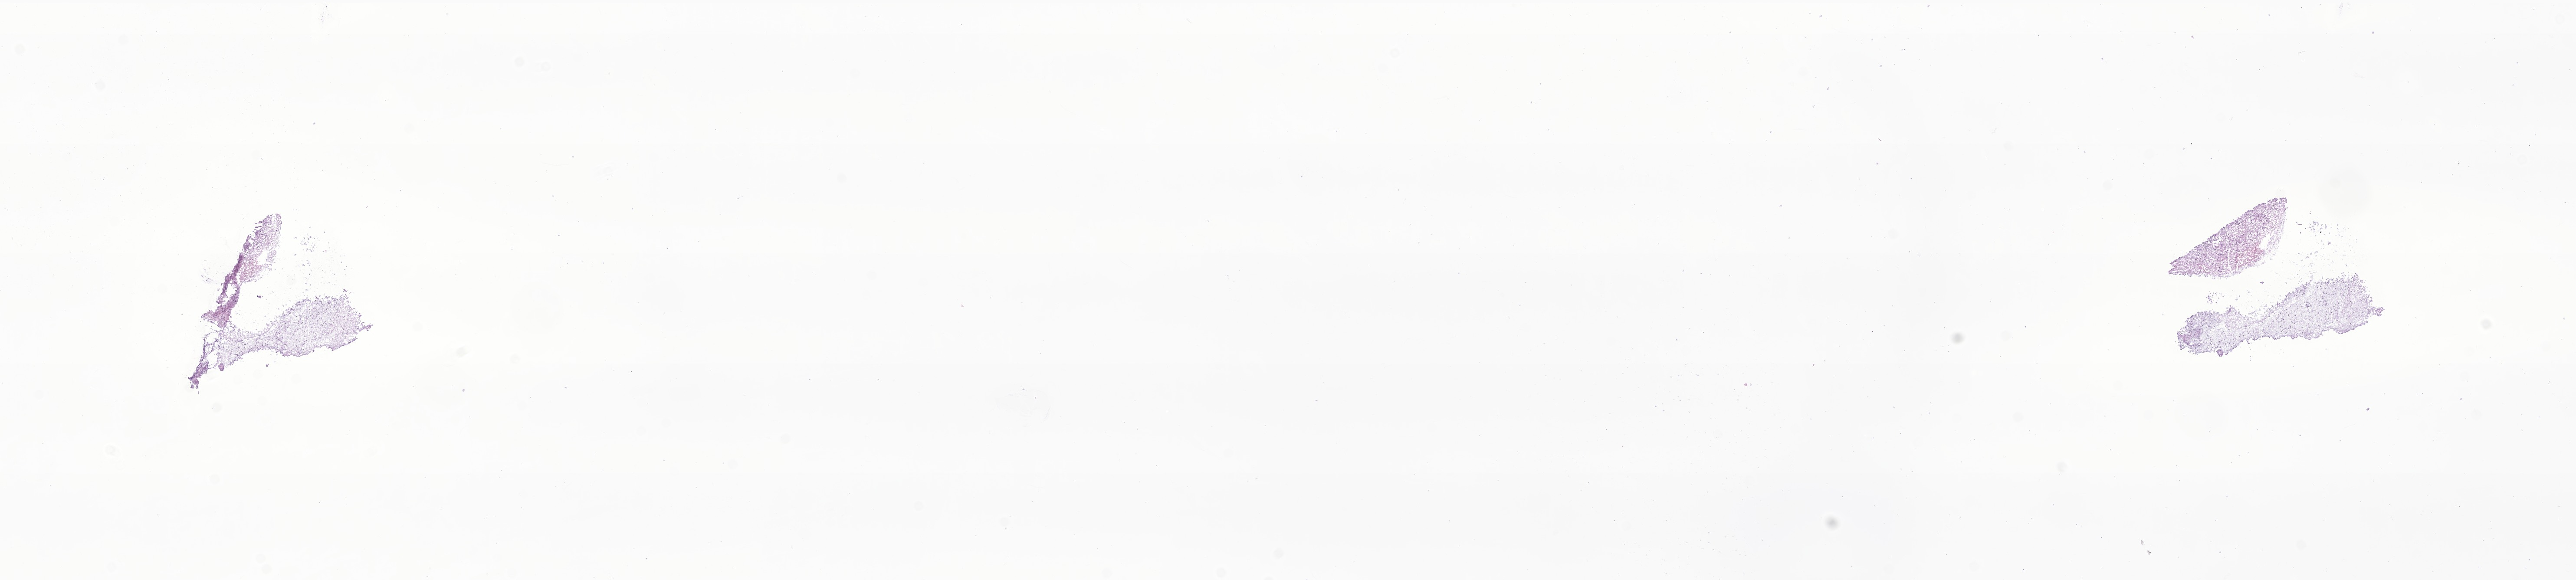
Digitized H&E-stained section of tumor tissue from the brain, low-resolution overview of the scanned area, about 25.0 x 5.6 mm, frozen section. Patient: female, age 74 months (6 years 2 months).
* diagnosis: Glioma, malignant